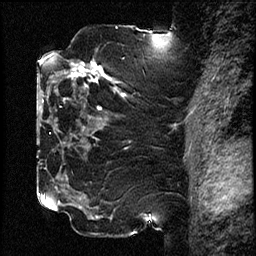
Breast MRI (dynamic contrast-enhanced), one sagittal slice. Position 47 of 78 along the scan axis. Dynamic contrast-enhanced study with each time point stored as its own series, time point 2 of 3 at this slice position (early post-contrast, ordered by acquisition time). 1.5 T. TE 4.2 ms, TR 17.6 ms. 2 mm slice thickness. 256 × 256 image matrix, field of view 200 × 200 mm. Patient: female, 42 years. Case-level facts recorded for this patient, not image findings: setting: breast cancer imaged before/during neoadjuvant chemotherapy; receptor status: HER2-positive.
Outlined on this slice (semi-automatic segmentation, software-assisted and operator-edited):
- analysis volume of interest (the breast-tissue region the enhancement analysis was run in; not a lesion): bounding box <50,51,126,129> (left, top, right, bottom; pixels)
- tumour enhancement mask (voxels above the 100 % enhancement threshold inside the analysis volume of interest): <71,62,124,109>